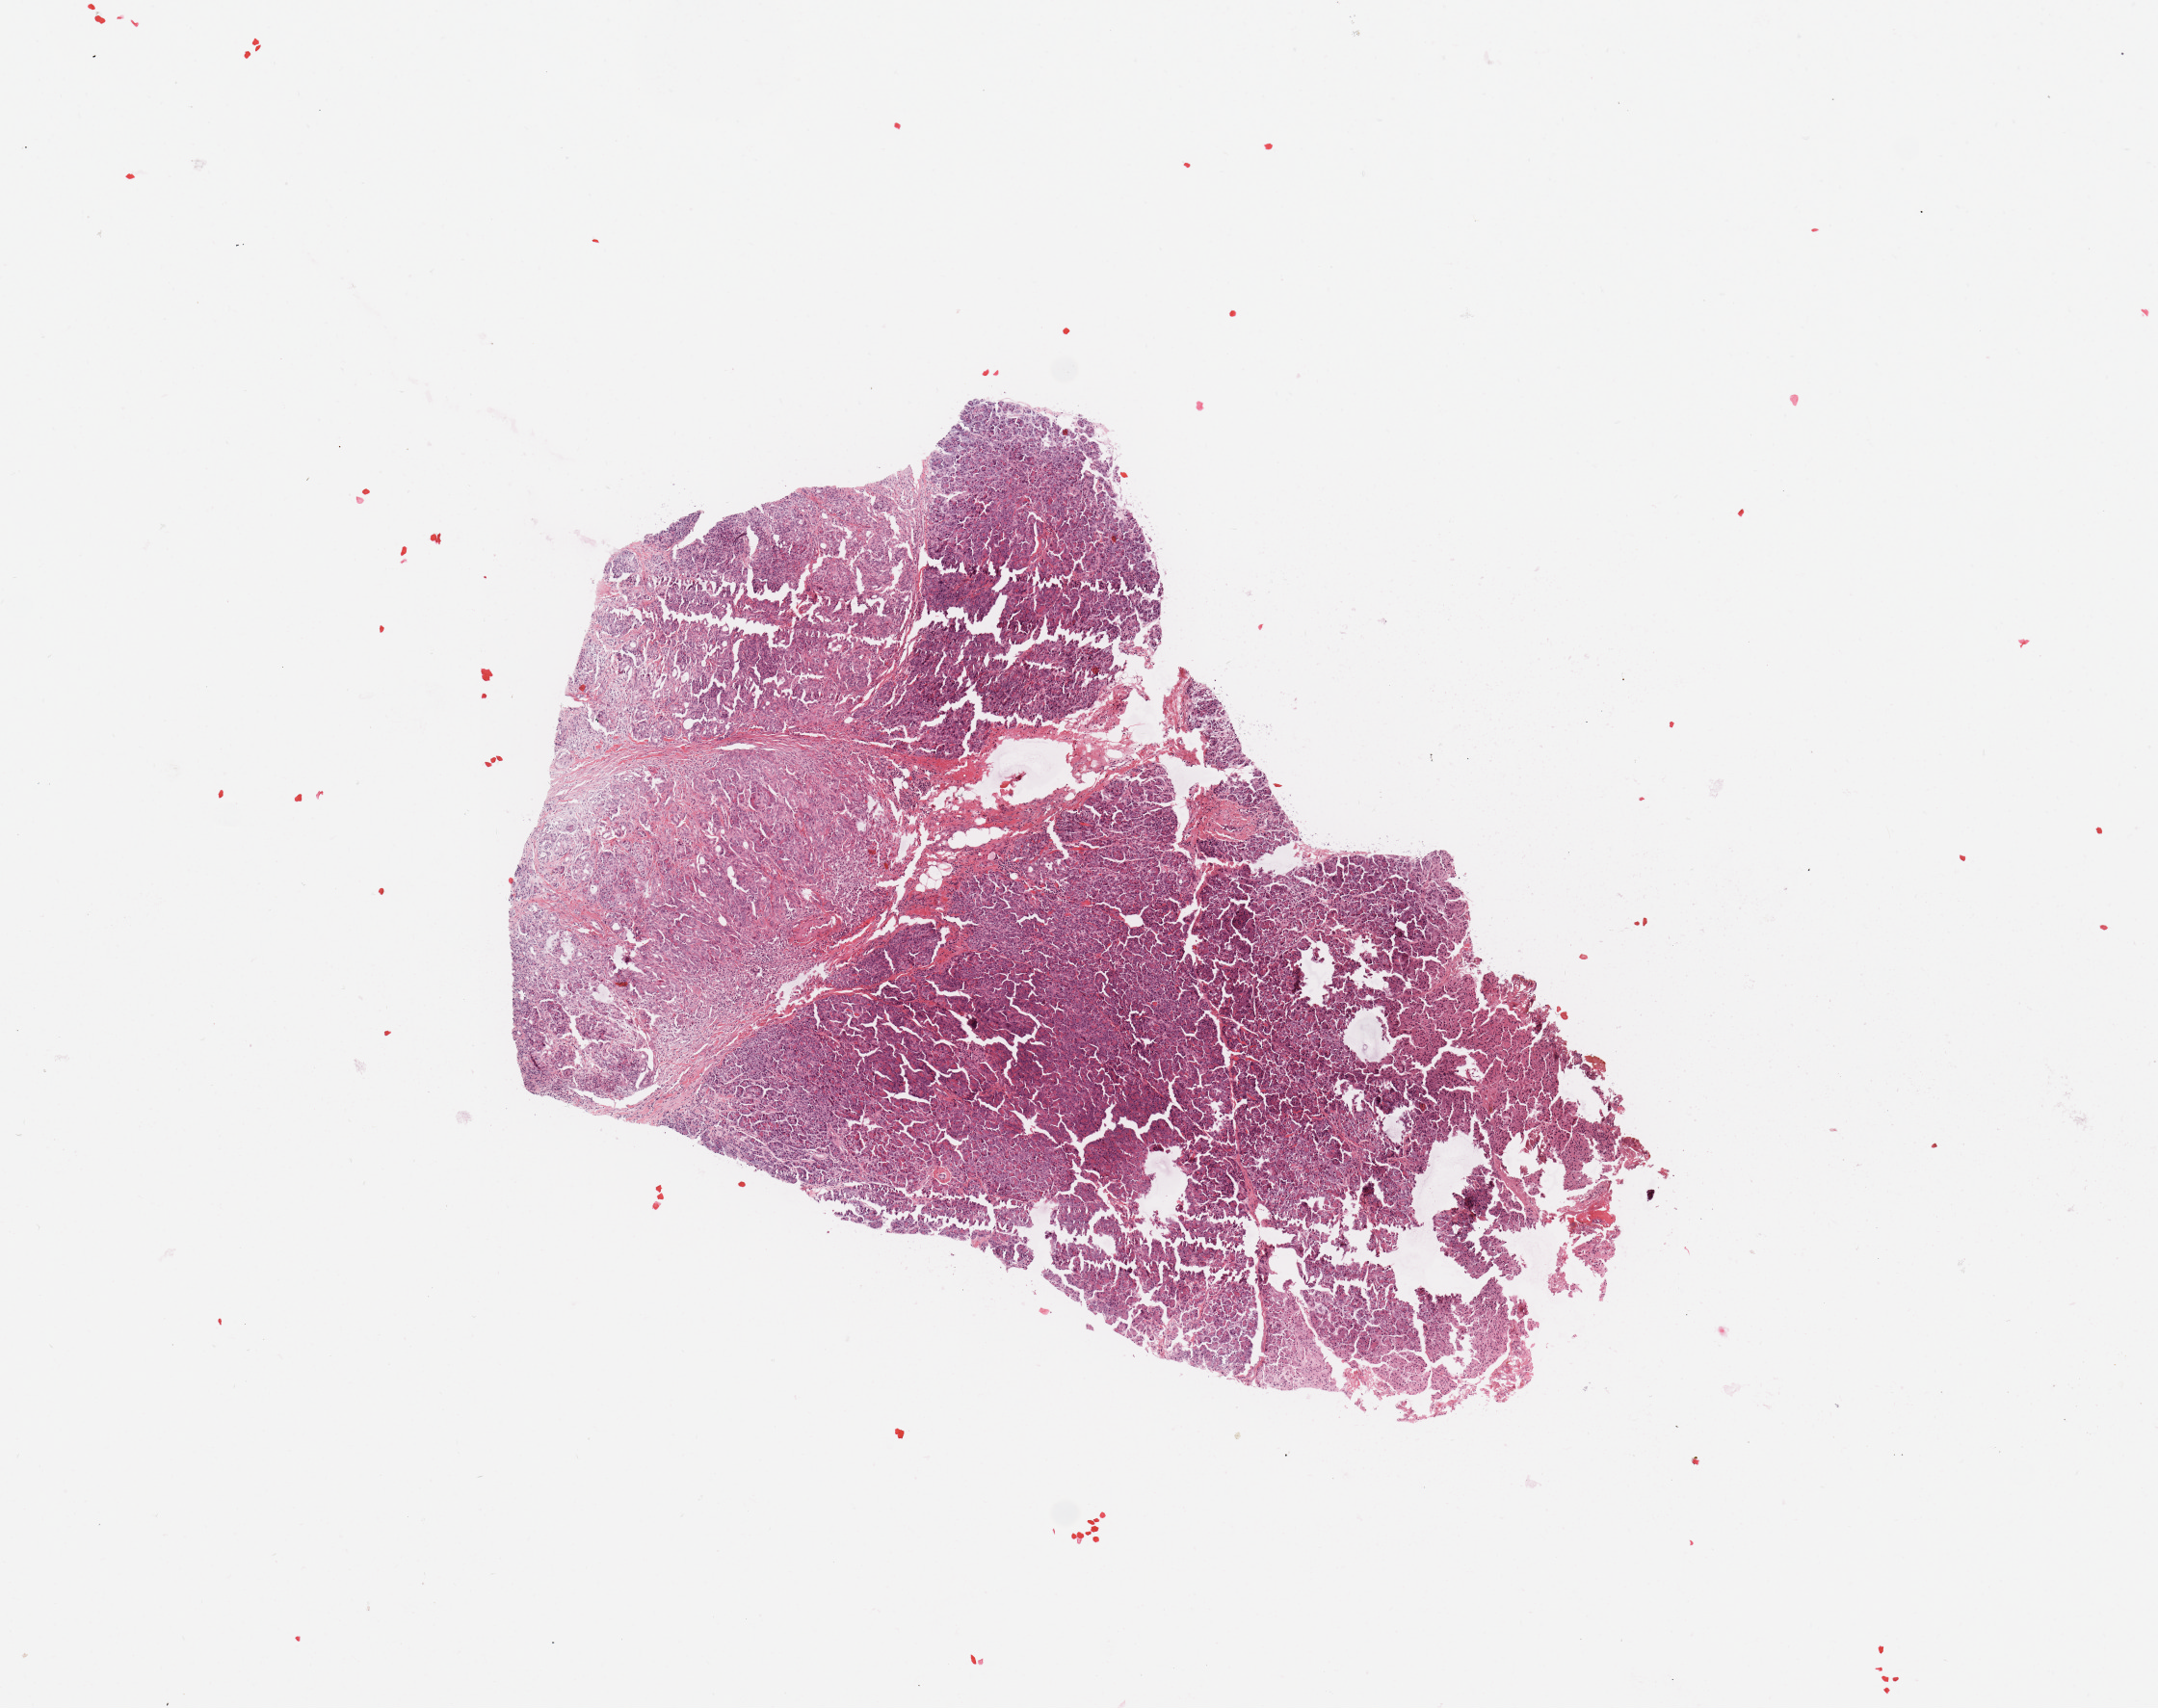
H&E-stained whole-slide image, shown as a low-resolution overview of the whole scanned area (about 8.9 x 7.0 mm, slide scanned at 20x); pancreas, tissue type not recorded.
Patient diagnosis (cohort enrolment): ductal adenocarcinoma (pancreas).